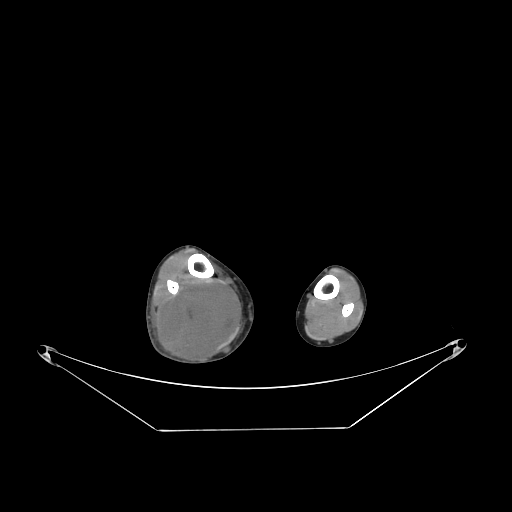
CT of an extremity soft-tissue mass (from a PET/CT study), one axial slice. Position 73 of 267 along the scan axis. 140 kVp. Soft-tissue window (W 400 / L 40 HU). 3.75 mm slice thickness. 512 × 512 image matrix, field of view 500 × 500 mm. Male patient. From the clinical record (not read from this slice): histological type: liposarcoma - round cell; grade: high; site of the primary tumour: right calf.
Annotated regions visible in this slice (expert contour drawn on MRI and transferred to this co-registered scan by the dataset authors):
- gross tumour volume (mass): bounding box [x1, y1, x2, y2] px = [158, 279, 241, 366]